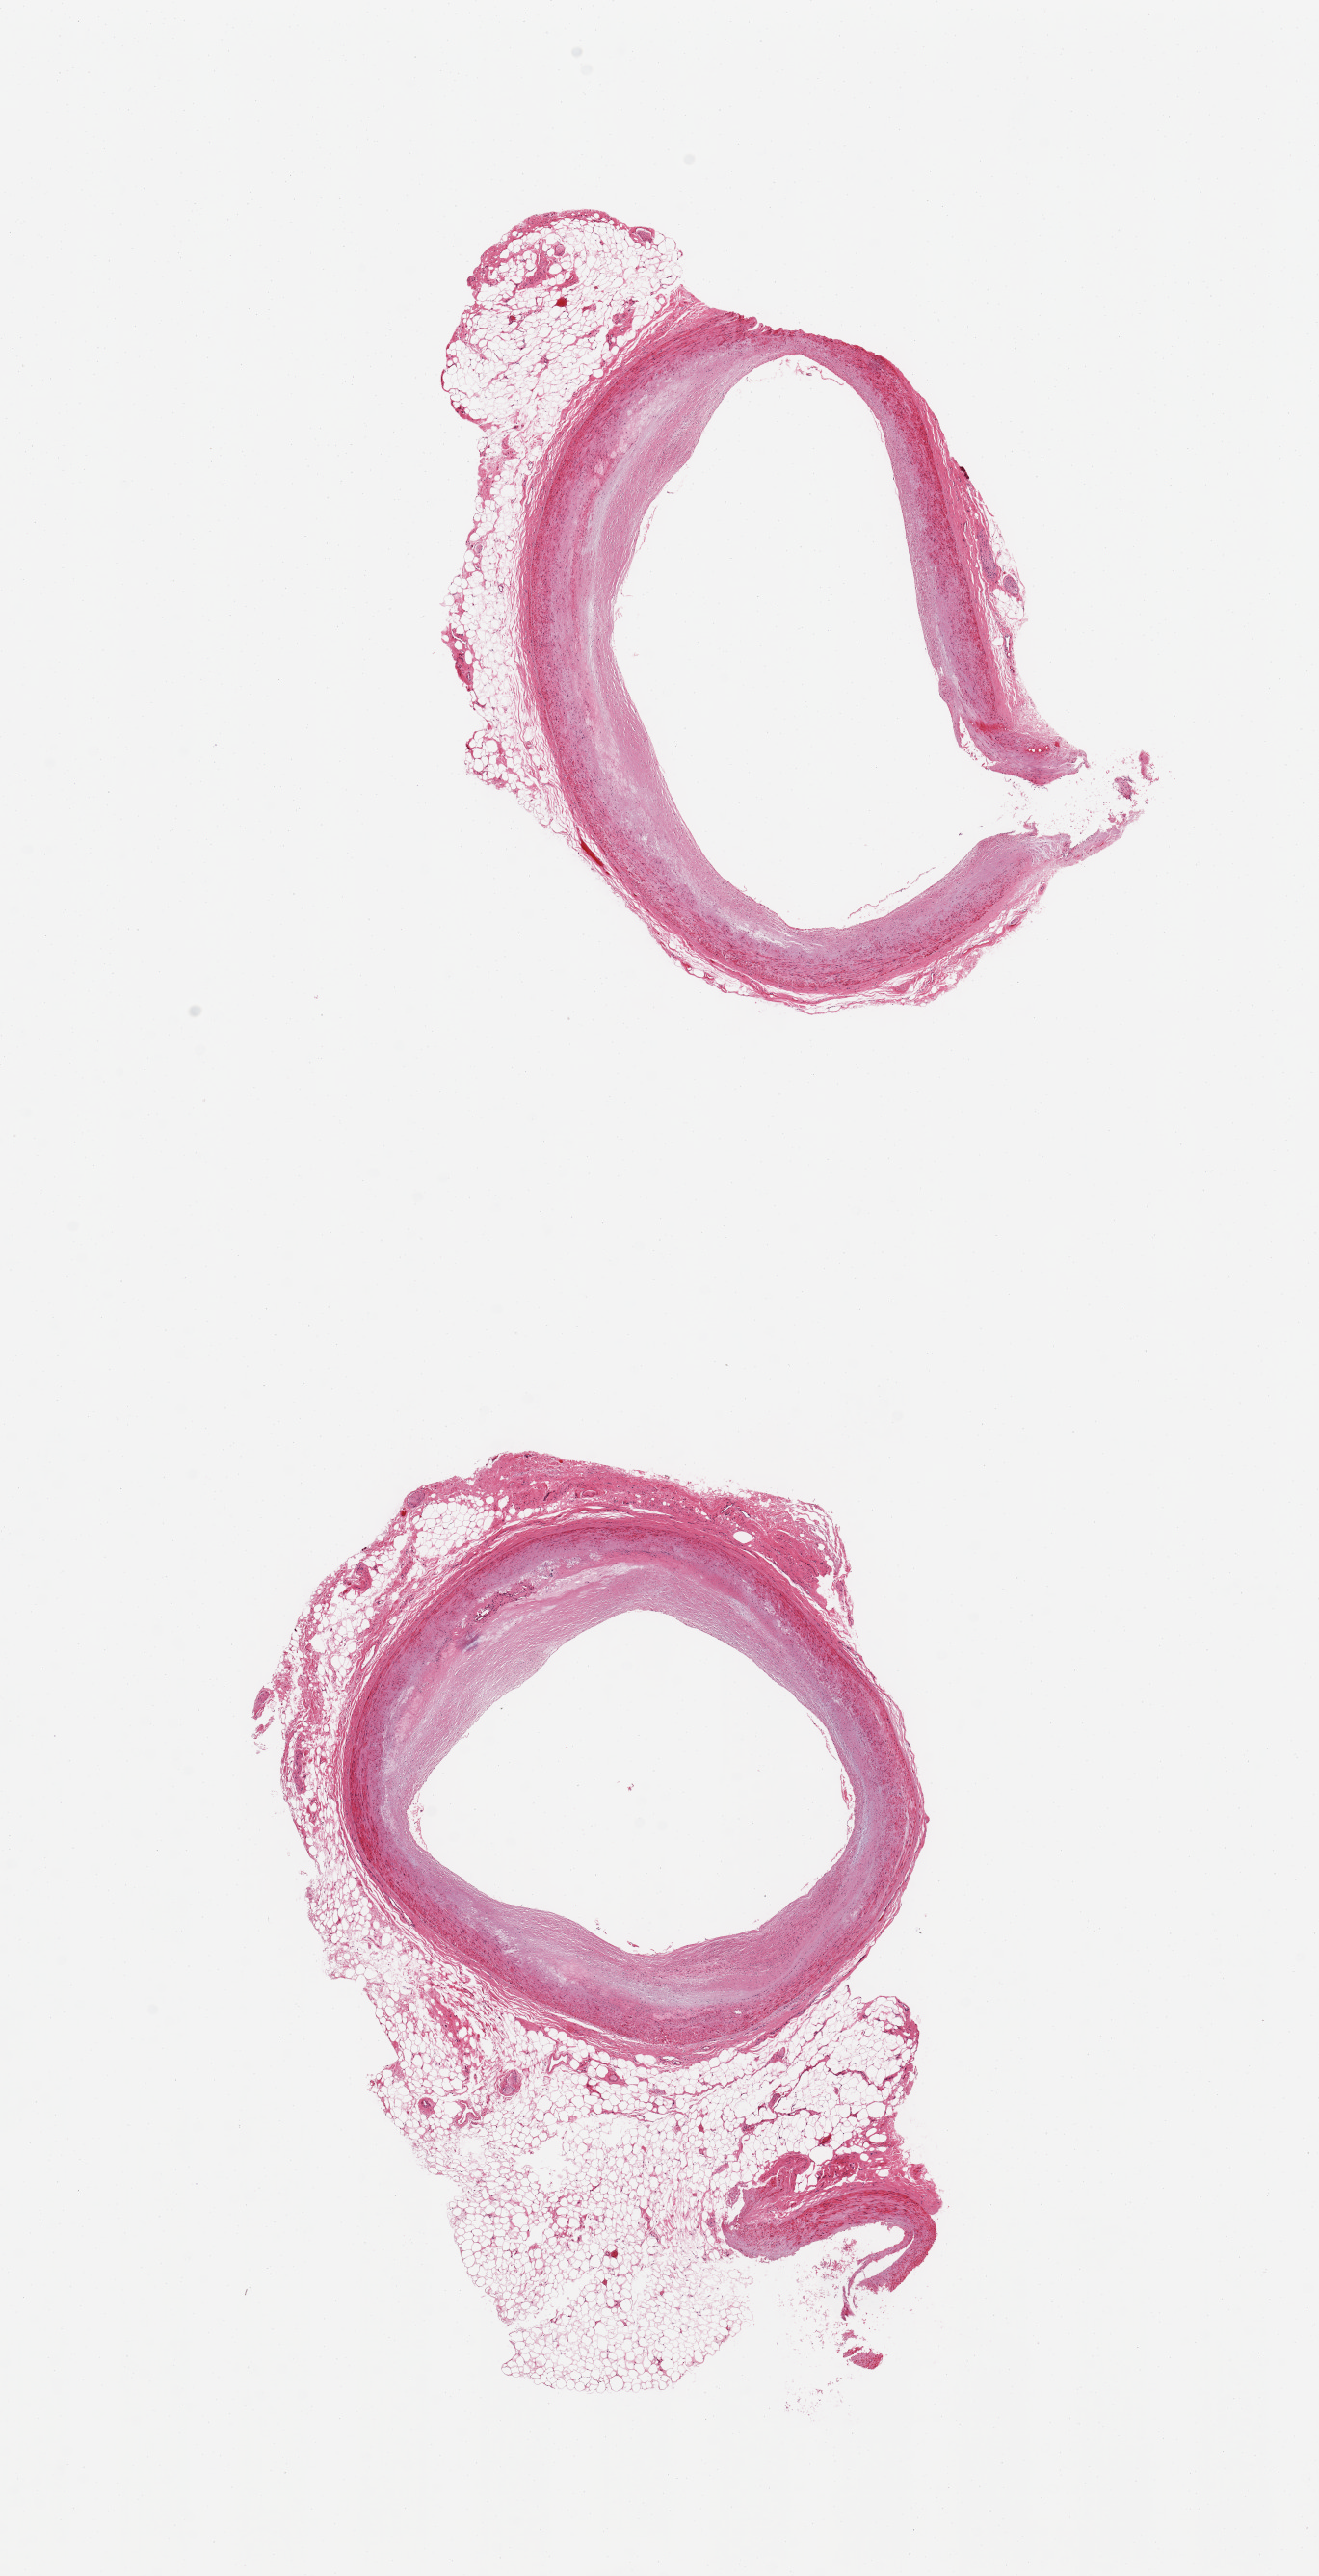
Haematoxylin and eosin whole-slide image, brightfield, whole scanned area (about 10.8 x 21.2 mm, from a 20x scan) shown as a low-resolution overview, PAXgene-fixed, paraffin-embedded tissue, target tissue: coronary artery, donor tissue sample. Donor: male.
Review note (as recorded): 2 pieces, partial rims of fat up to ~2.5mm, atherosis is ~20-30% occlusive, up to ~0.5mm layer.